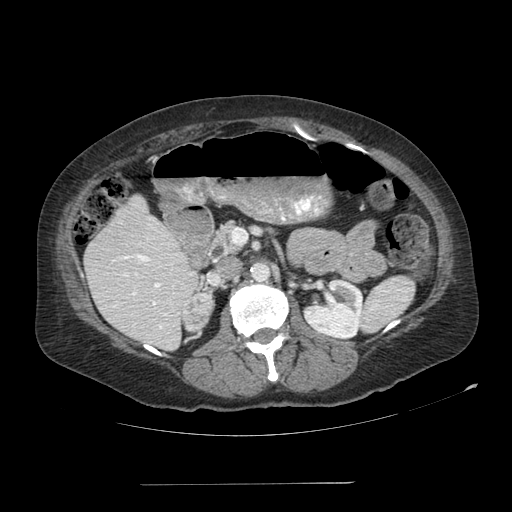
Contrast-enhanced abdominal CT, one axial slice; slice 51 of 113 in the series (ordered by position); 120 kVp; soft-tissue window (W 400 / L 40 HU); 512 × 512 image matrix, field of view 440 × 440 mm. Female patient, age 67 years. From the clinical record (not read from this slice): diagnosis: adrenocortical carcinoma; tumour side: right adrenal; tumour size at pathology: 9.8 cm; Ki-67 index: 59 %; stage (as recorded): 4.
Structures marked on this image (semi-automatically segmented with operator editing):
- mass: box from (x=183, y=294) to (x=214, y=331) px